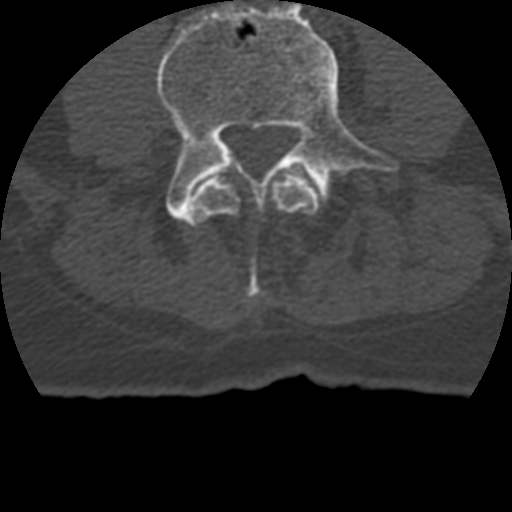
CT including the spine, one axial slice; position 72 of 399 along the scan axis; reconstruction kernel STANDARD; 120 kVp; bone window (W 1800 / L 400 HU); 1.25 mm slice thickness; 512 × 512 image matrix, field of view 160 × 160 mm. Patient age 69 years. Case-level facts recorded for this patient, not image findings: primary cancer: prostate.
Outlined on this slice (semi-automatically segmented with operator editing):
- L3 vertebra: bounding box (x1, y1, x2, y2) in pixels: (192, 174, 319, 299)
- L4 vertebra: (157, 0, 400, 225)